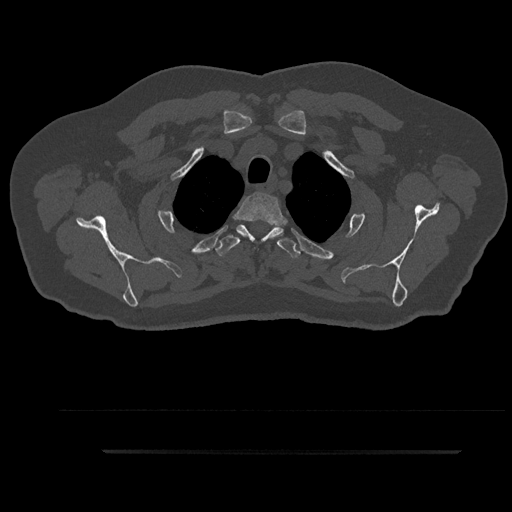
CT including the spine, one axial slice. Slice 739 of 797 in the series (ordered by position). Reconstruction kernel Br40s/3. 120 kVp. Bone window (W 1800 / L 400 HU). 0.5 mm slice thickness. 512 × 512 image matrix, field of view 432 × 432 mm. Patient: male, 63 years. From the clinical record (not read from this slice): primary cancer: renal.
Outlined on this slice (semi-automatic segmentation, software-assisted and operator-edited):
- T2 vertebra: bounding box <237,192,284,244> (left, top, right, bottom; pixels)
- T3 vertebra: <215,224,301,258>